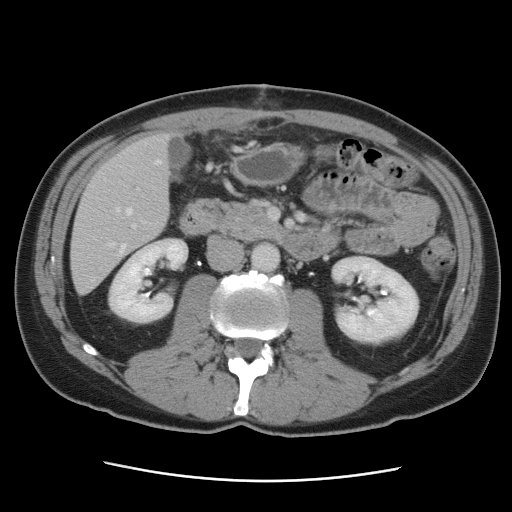
Contrast-enhanced abdominal CT, one axial slice. Slice 32 of 89 in the series (ordered by position). Soft-tissue window (W 400 / L 40 HU). 512 × 512 image matrix, field of view 366 × 366 mm. Male patient, age 59 years. Case-level facts recorded for this patient, not image findings: diagnosis: colorectal cancer liver metastases, imaged before liver resection; multiple liver metastases: yes; largest metastasis: 0.6 cm.
Structures marked on this image (manually delineated by an expert):
- hepatic veins: bounding box [x1, y1, x2, y2] px = [108, 160, 161, 256]
- liver: [72, 135, 169, 293]
- planned liver remnant (the part of the liver to remain after resection): [73, 134, 169, 245]
- portal vein (with intrahepatic branches): [133, 224, 136, 228]